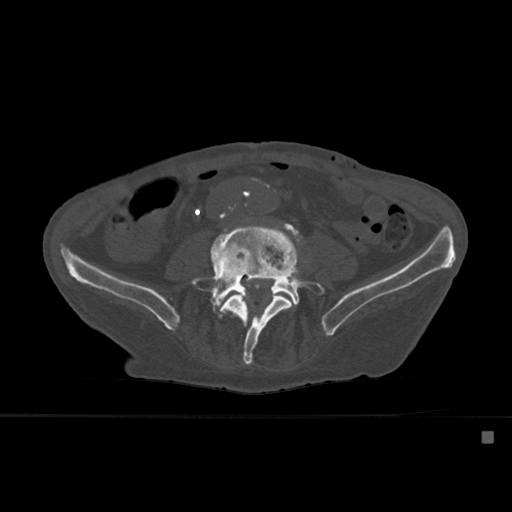
CT including the spine, one axial slice; position 185 of 527 along the scan axis; bone window (W 1800 / L 400 HU); 1.5 mm slice thickness; 512 × 512 image matrix, field of view 373 × 373 mm. Patient: male, 78 years. From the clinical record (not read from this slice): primary cancer: prostate.
Structures marked on this image (semi-automatically segmented with operator editing):
- L4 vertebra: bounding box <220,265,299,365> (left, top, right, bottom; pixels)
- L5 vertebra: <190,227,325,319>